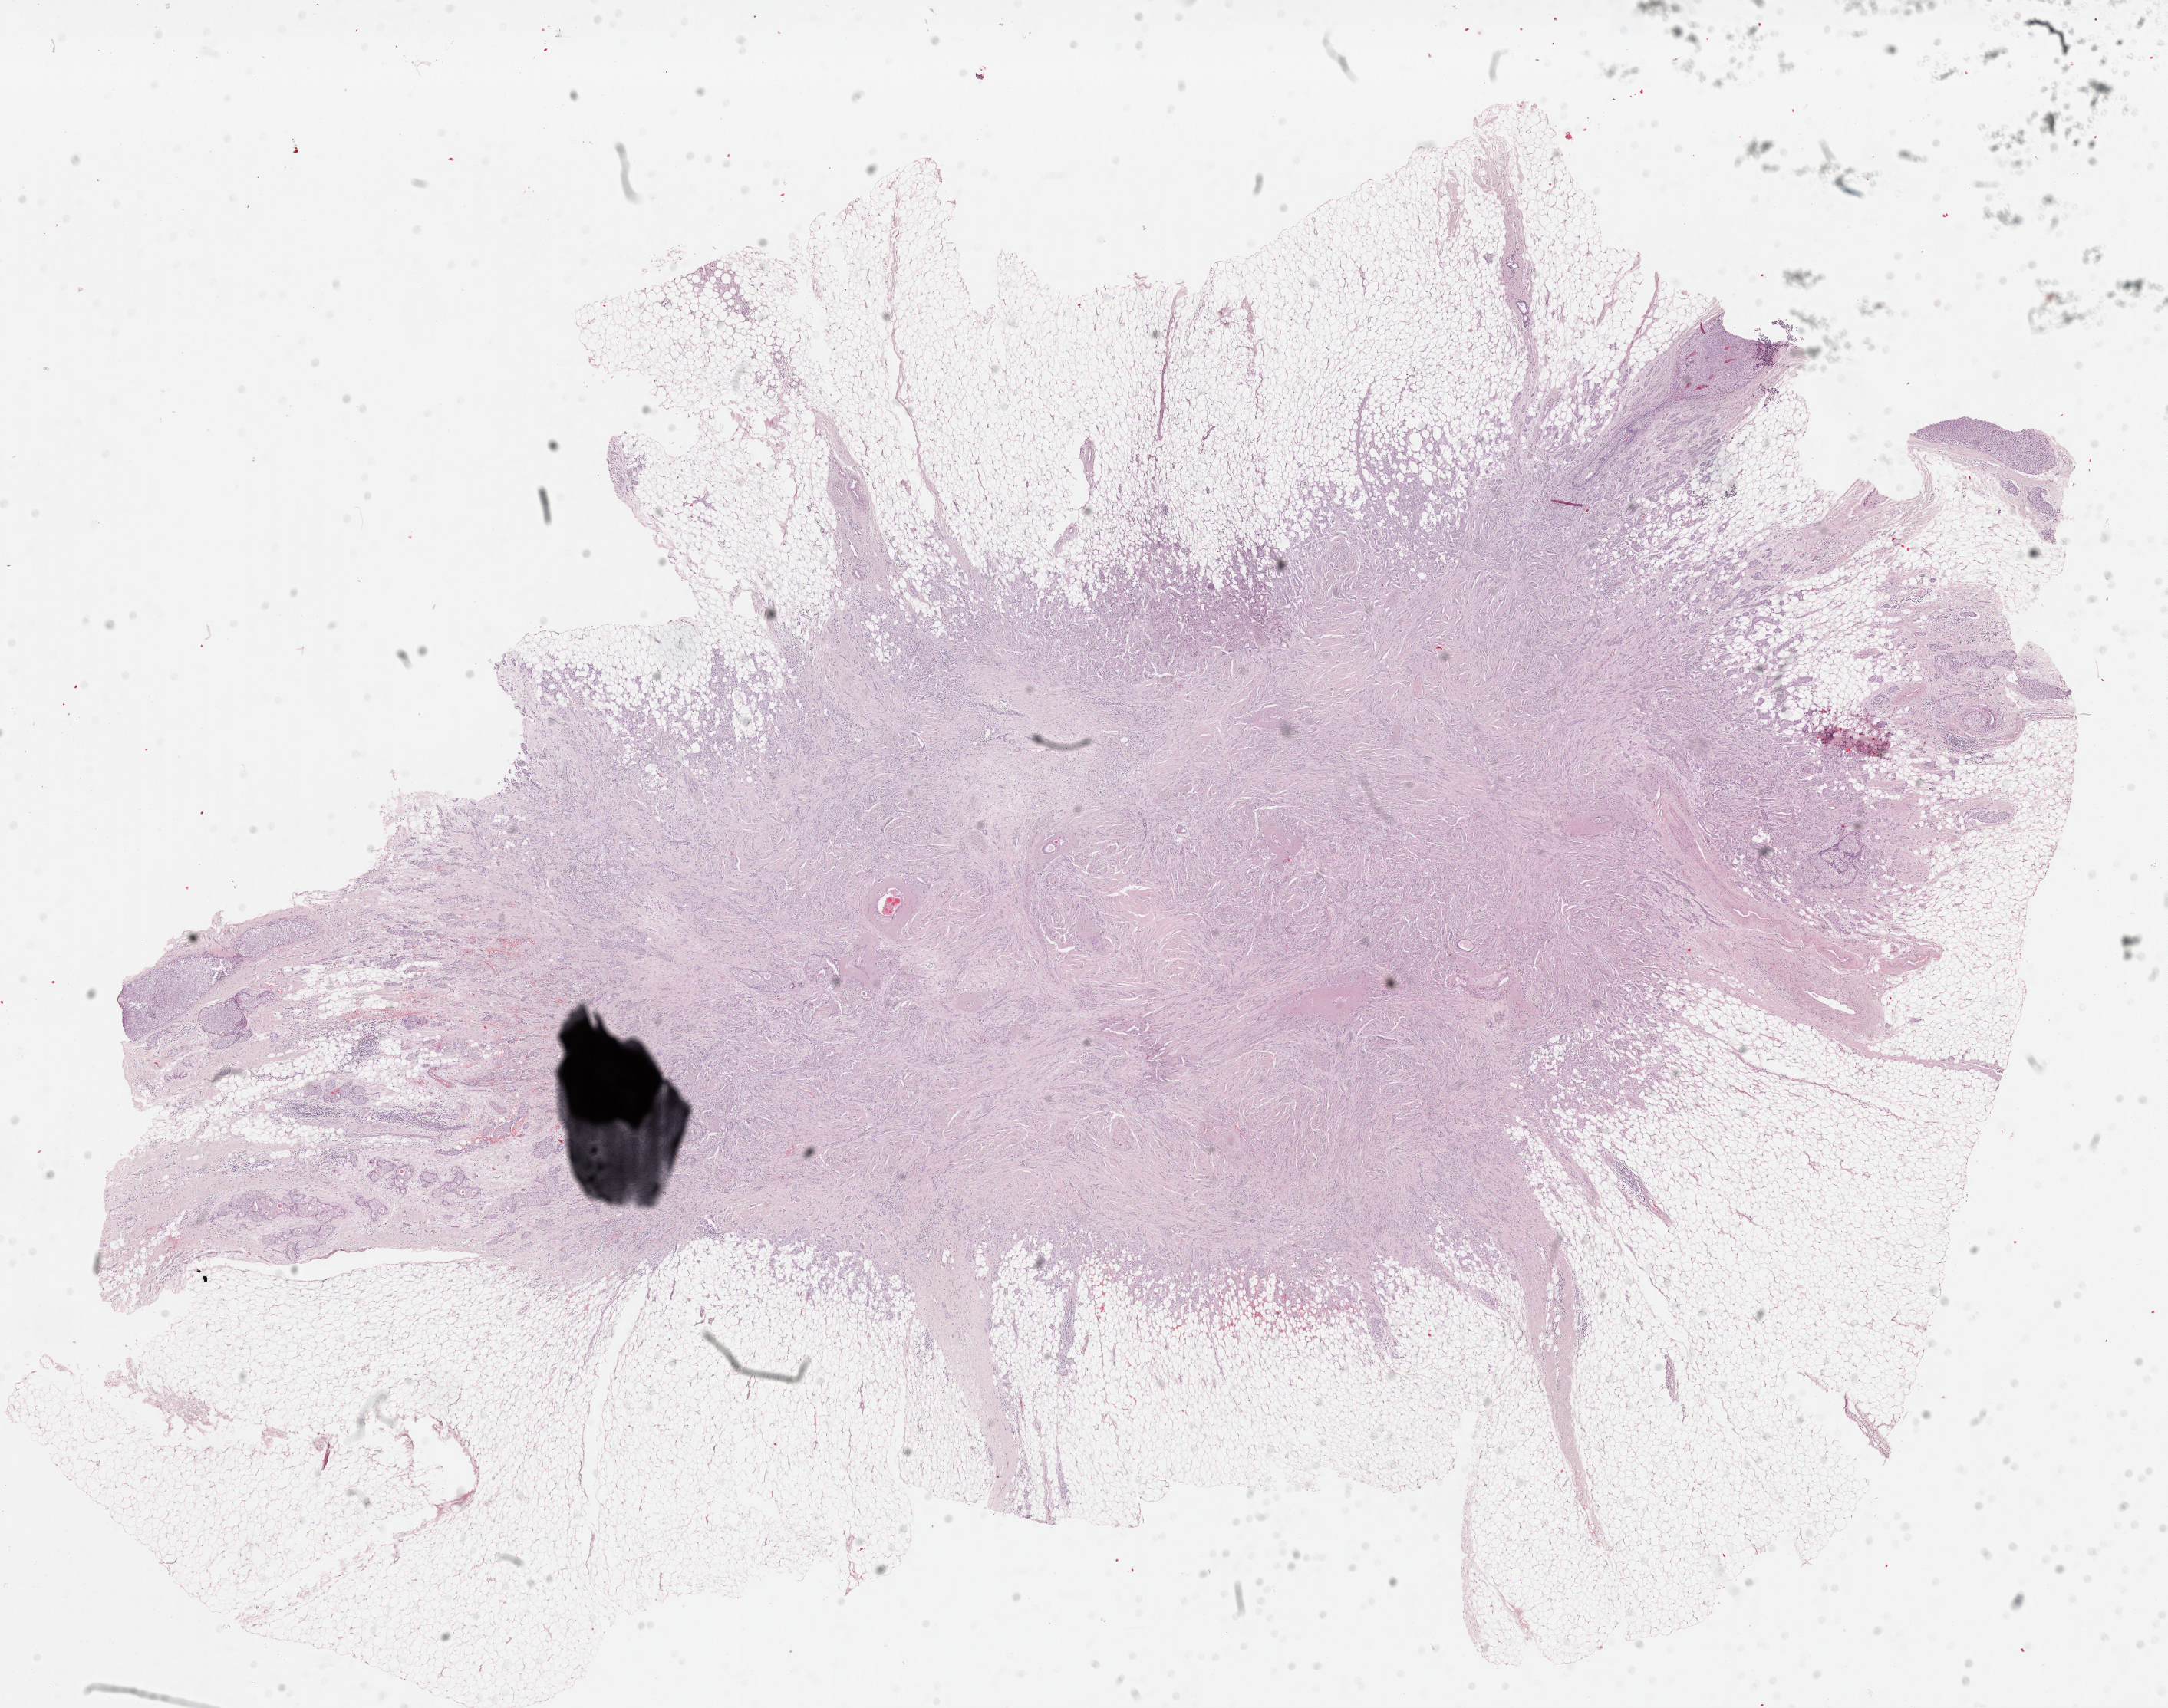
Digitized H&E tissue section (whole slide) — a low-resolution overview of the entire scanned area, about 22.3 x 17.6 mm (slide scanned at 40x); formalin-fixed paraffin-embedded (FFPE) diagnostic section; sample: primary tumour, breast. Female, age 56 years at initial diagnosis.
AJCC pathologic stage: IA (7th edition). TNM: T1c N0 M0. Lymph nodes positive (case pathology): 0 of 1 examined. Laterality: left. Pathologic diagnosis: Infiltrating duct carcinoma, NOS.